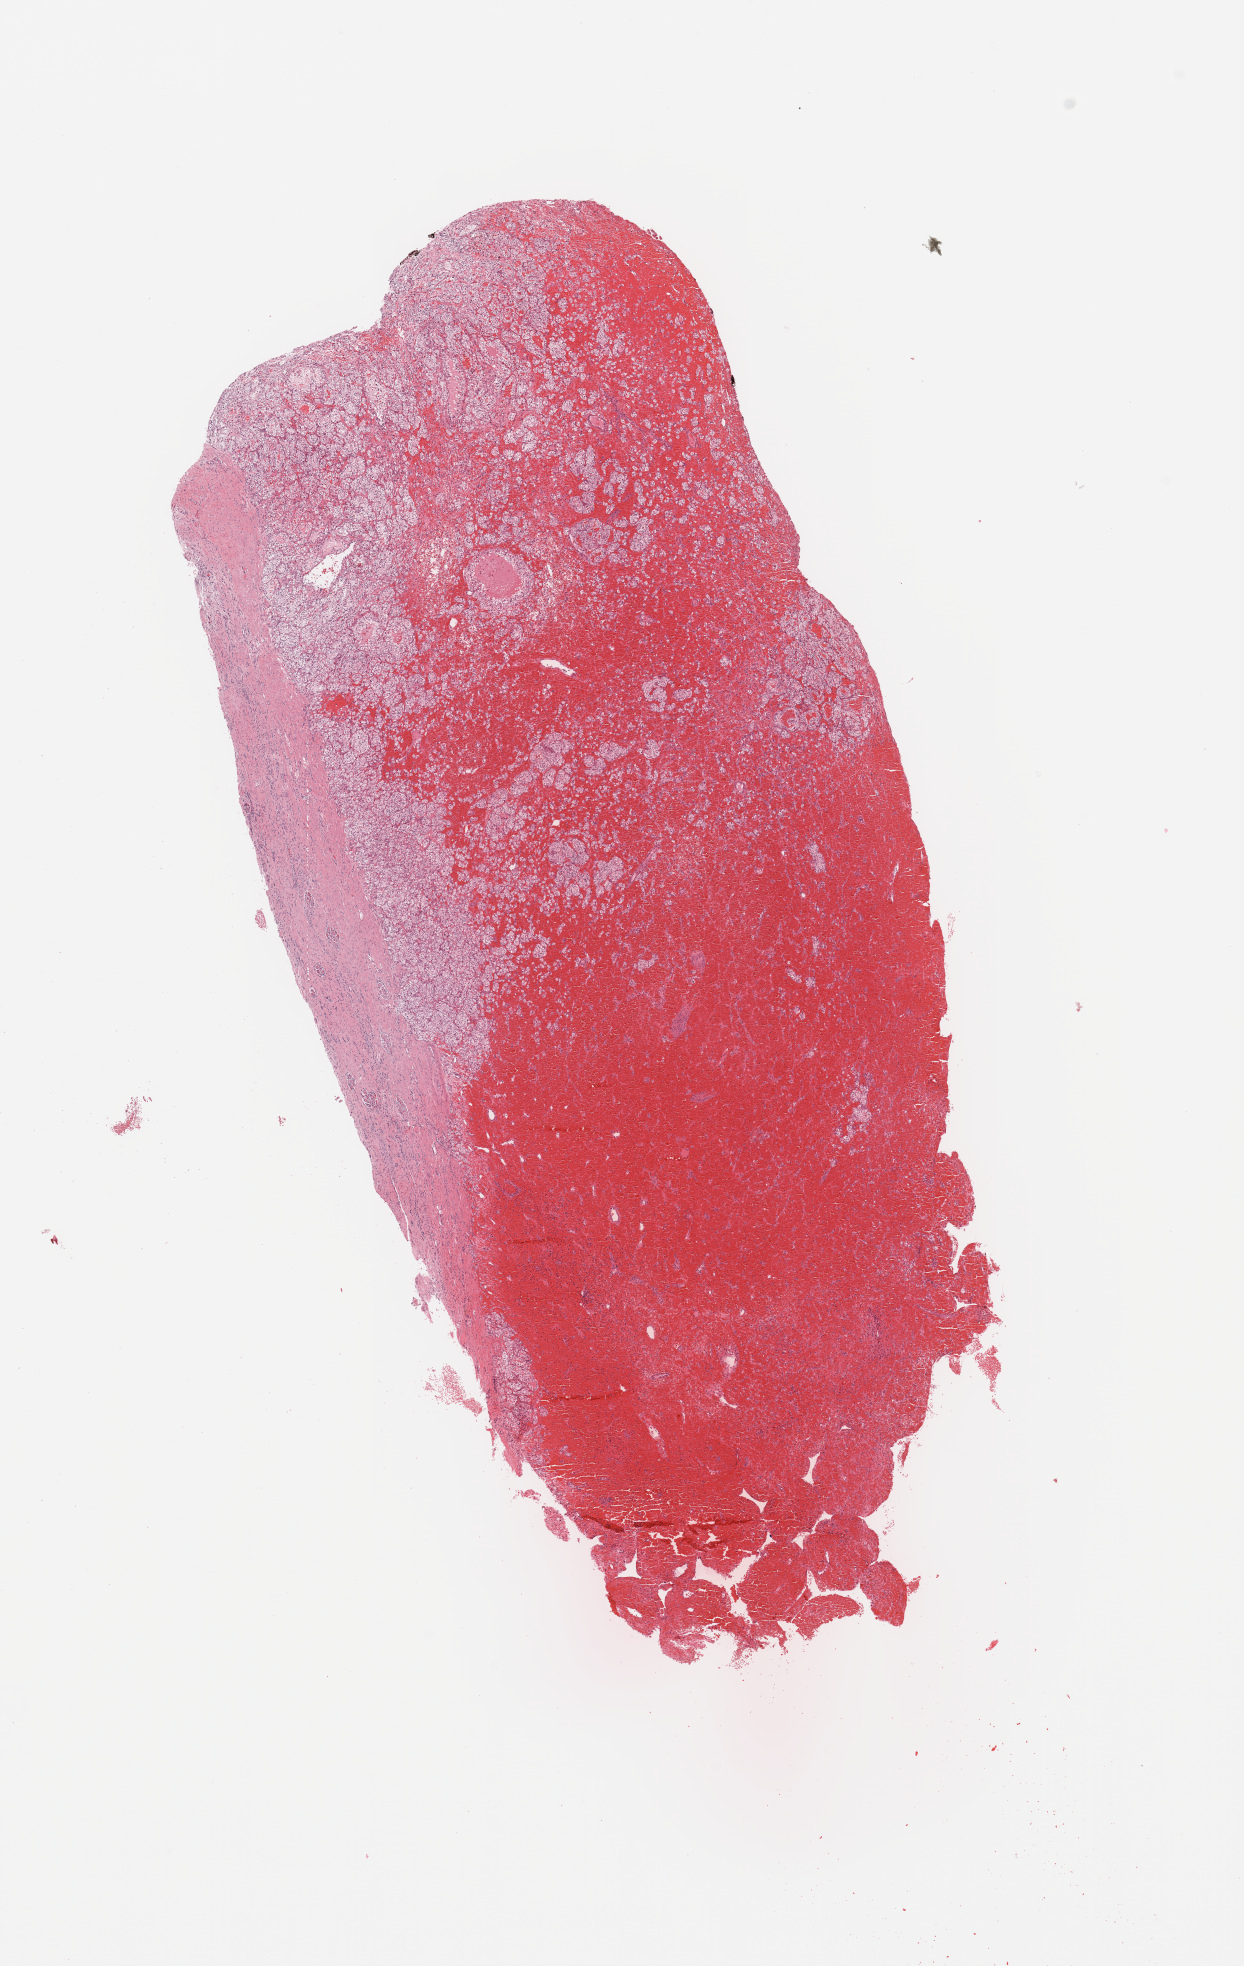
H&E-stained whole-slide image, low-resolution overview of the scanned area, about 9.8 x 15.6 mm (slide scanned at 20x); tumour tissue sample, sampled site: kidney. Patient: female, age 57 years. Histologic grade: G2 (moderately differentiated). Composition of this section per pathologist review: tumour nuclei 80%, necrosis 10%.
Histologic diagnosis: Renal cell carcinoma, NOS. Primary tumour site (as recorded): upper pole. AJCC pathologic stage: I.